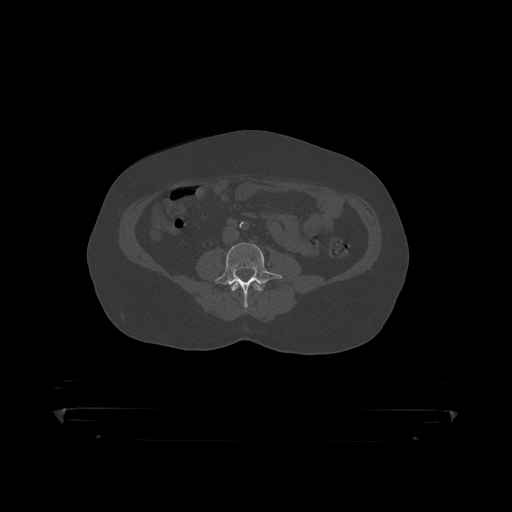
CT including the spine, one axial slice. Position 68 of 390 along the scan axis. Reconstruction kernel STANDARD. Bone window (W 1800 / L 400 HU). 1.25 mm slice thickness. 512 × 512 image matrix. Patient: male, 60 years. Case-level facts recorded for this patient, not image findings: primary cancer: prostate.
Structures marked on this image (semi-automatically segmented with operator editing):
- L3 vertebra: box from (x=231, y=282) to (x=263, y=308) px
- L4 vertebra: (x=210, y=243)–(x=283, y=306)